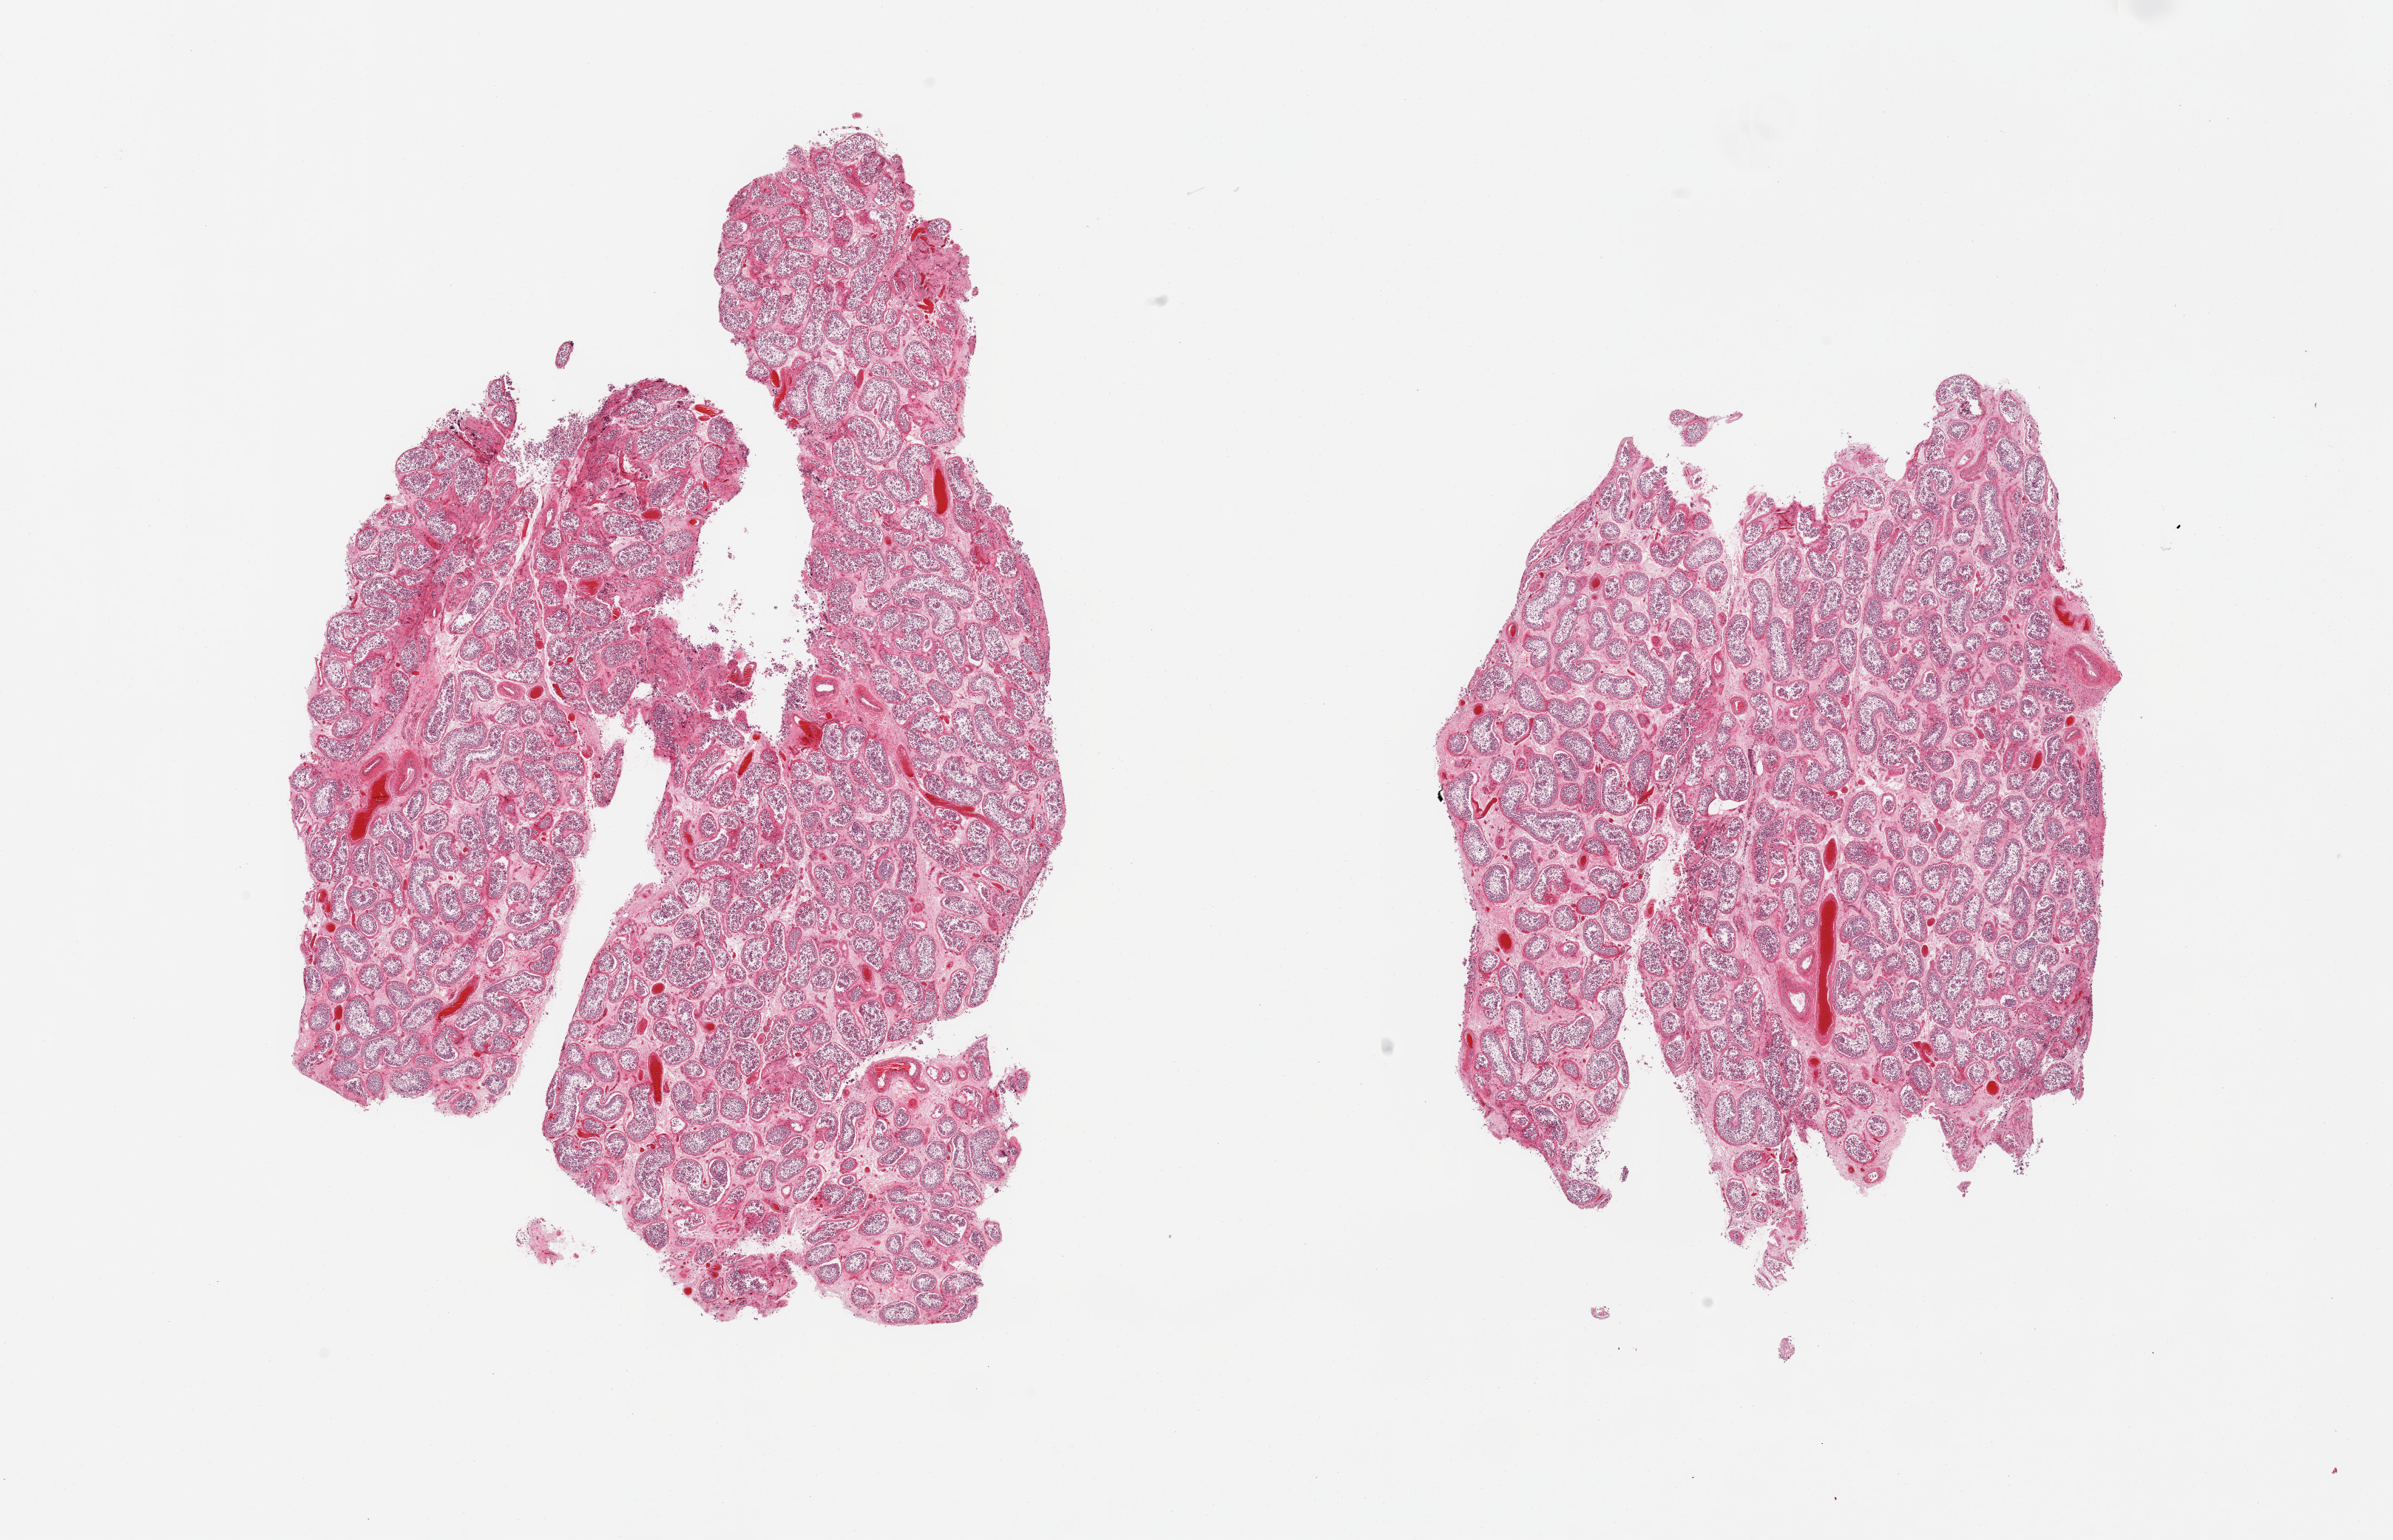
Hematoxylin and eosin (H&E) whole-slide image, a low-resolution overview of the entire scanned area, about 25.6 x 16.5 mm (slide scanned at 20x), PAXgene-fixed, paraffin-embedded tissue, section of testis (target tissue), donor tissue sample. Donor: male.
• review note (as recorded): 2 pieces; spermatogenesis